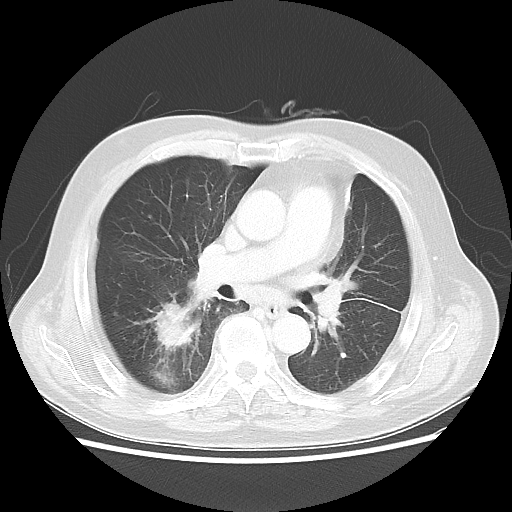
Chest CT, one axial slice. Slice 21 of 44 in the series (ordered by position). Lung window (W 1500 / L -600 HU). 512 × 512 image matrix, field of view 359 × 359 mm. Male patient, age 83 years. From the clinical record (not read from this slice): clinical TNM (as recorded): T2 N3 M0.
Structures marked on this image (bounding box drawn by a radiologist):
- lung tumour (recorded histology: adenocarcinoma): bounding box <144,286,200,359> (left, top, right, bottom; pixels)